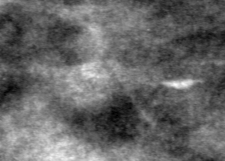
Cropped region of a digitized screen-film mammogram centred on a radiologist-marked abnormality; left breast; CC view.
- Calcifications, morphology fine linear branching, distribution linear; BI-RADS assessment category 4; pathology result (as recorded, not read from the image): malignant.